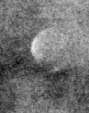
Cropped region of a digitized screen-film mammogram centred on a radiologist-marked abnormality; right breast; CC view.
Marked abnormality: calcifications, morphology lucent center; BI-RADS assessment category 2; subtlety rating 3 on a 1 (subtle) to 5 (obvious) scale; benign; no additional work-up was recommended (benign without callback).